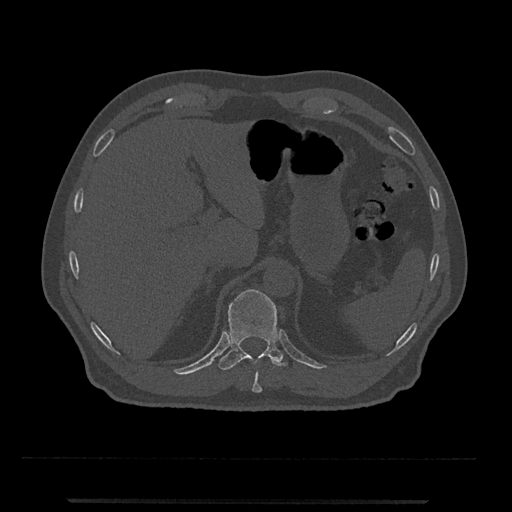
CT including the spine, one axial slice; slice 477 of 797 in the series (ordered by position); bone window (W 1800 / L 400 HU); 512 × 512 image matrix. Male patient, age 63 years. From the clinical record (not read from this slice): primary cancer: prostate.
Structures marked on this image (semi-automatic segmentation, software-assisted and operator-edited):
- T10 vertebra: box from (x=252, y=371) to (x=262, y=393) px
- T11 vertebra: (x=218, y=289)–(x=287, y=370)